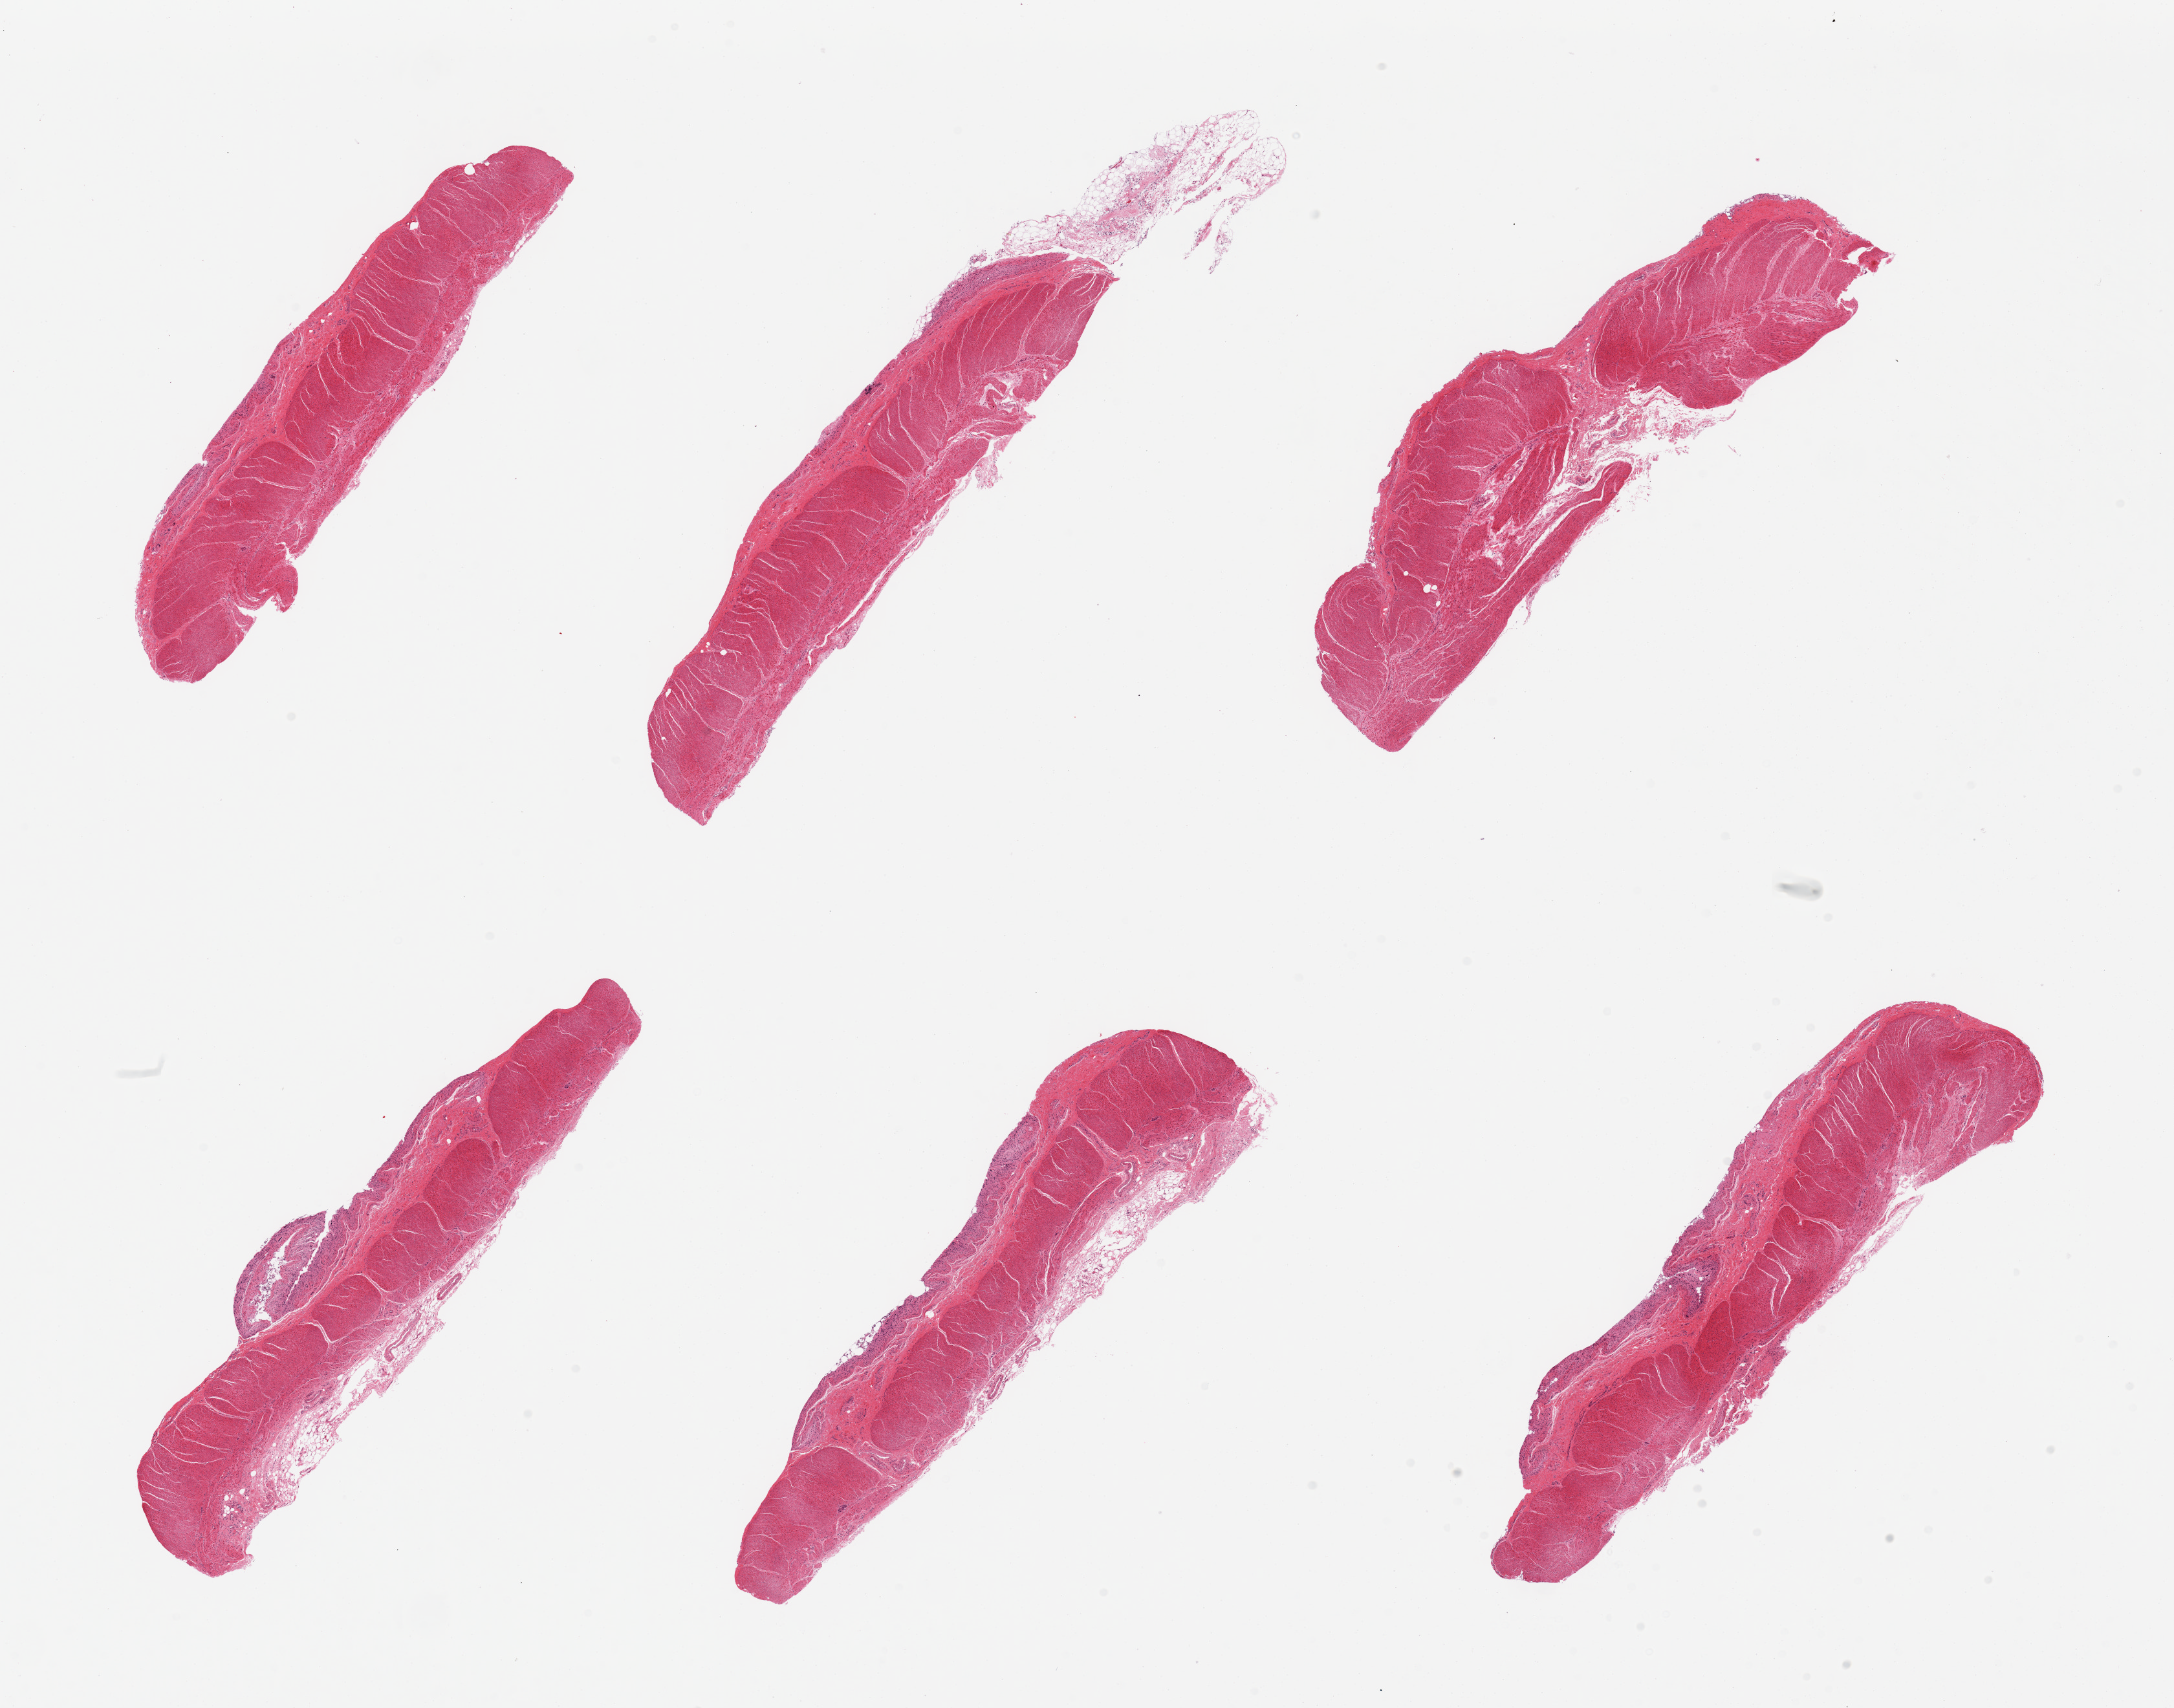
Digitized H&E-stained section — whole scanned area (about 26.6 x 20.9 mm) shown as a low-resolution overview. PAXgene-fixed paraffin-embedded (PFPE) section. Section of sigmoid colon (target tissue). Donor tissue sample. Female donor.
Reviewer comment on this tissue sample: 6 pieces, adherent fat/serosa ~0.5mm.